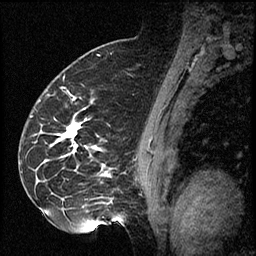
Breast MRI (dynamic contrast-enhanced), one sagittal slice; position 44 of 60 along the scan axis; dynamic contrast-enhanced series, image 2 of 2 at this slice position (ordered by acquisition); 1.5 T; TE 4.2 ms, TR 17.3 ms; 2 mm slice thickness; 256 × 256 image matrix. Female patient. From the clinical record (not read from this slice): setting: breast cancer imaged before/during neoadjuvant chemotherapy; receptor status: HR-positive, HER2-negative.
Annotated regions visible in this slice (semi-automatic segmentation, software-assisted and operator-edited):
- analysis volume of interest (the breast-tissue region the enhancement analysis was run in; not a lesion): box from (x=41, y=93) to (x=115, y=223) px
- tumour enhancement mask (voxels above the 100 % enhancement threshold inside the analysis volume of interest): (x=66, y=124)–(x=81, y=152)